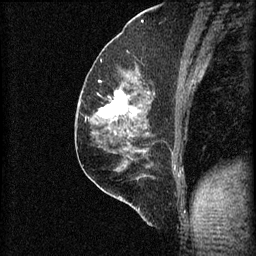
Breast MRI (dynamic contrast-enhanced), one sagittal slice; slice 34 of 60 in the series (ordered by position); 3 images stored at this slice position (order not interpretable as contrast timing); 1.5 T; TE 4.2 ms, TR 8.2 ms; 2 mm slice thickness; 256 × 256 image matrix, field of view 180 × 180 mm. Female patient, age 59 years.
Annotated regions visible in this slice (semi-automatic segmentation, software-assisted and operator-edited):
- analysis volume of interest (the breast-tissue region the enhancement analysis was run in; not a lesion): box from (x=92, y=74) to (x=155, y=131) px
- tumour enhancement mask (voxels above the 70 % enhancement threshold inside the analysis volume of interest): (x=99, y=80)–(x=150, y=119)